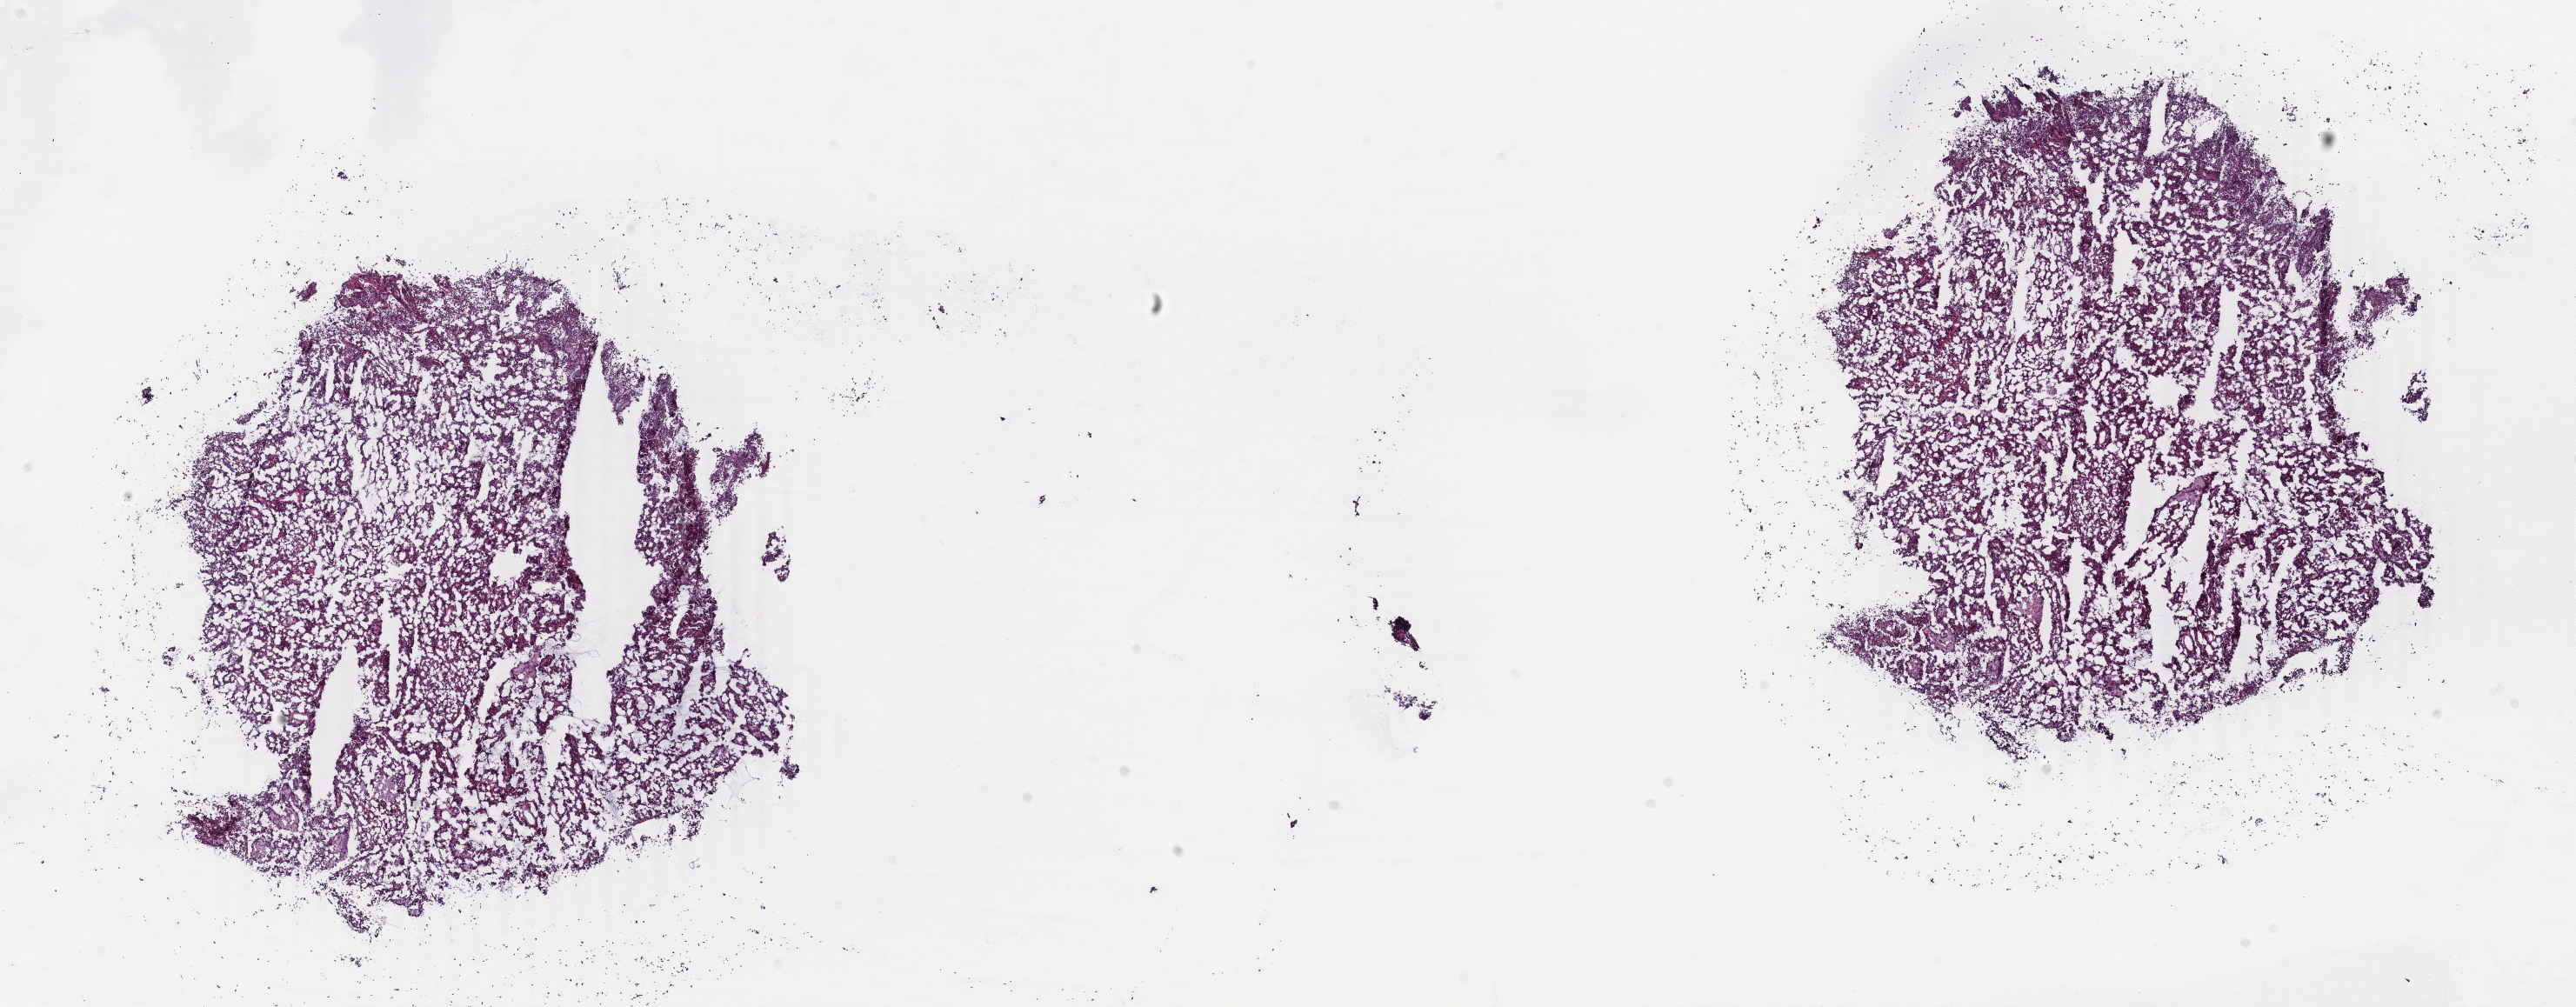
H&E whole-slide image, low-resolution overview of the scanned area, about 23.6 x 9.2 mm (from a 40x scan); frozen section; kidney, primary tumour sample. Patient: male, age at initial diagnosis 51 years. Pathologist review of this section (percent, as recorded): tumour cells 80%, tumour nuclei 90%, normal cells 0%, stromal cells 10%, necrosis 10%. Inflammatory infiltration, as recorded: lymphocyte infiltration 0%, monocyte infiltration 0%, neutrophil infiltration 0%.
TNM: T1a NX MX. Laterality: left. Pathologic diagnosis: Papillary adenocarcinoma, NOS. AJCC pathologic stage: I (7th edition).